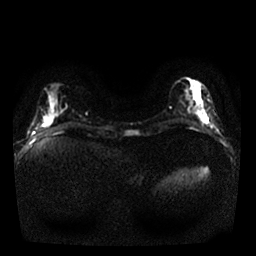
Breast MRI, one axial slice; position 10 of 25 along the scan axis; diffusion-weighted series; image 2 of 4 stored at this slice position (different b-values; order by instance number); 1.5 T; 4 mm slice thickness; 256 × 256 image matrix, field of view 320 × 320 mm. Female patient.
Structures marked on this image (outlined manually by an expert reader):
- tumour on diffusion-weighted imaging: bounding box (x1, y1, x2, y2) in pixels: (203, 116, 208, 123)